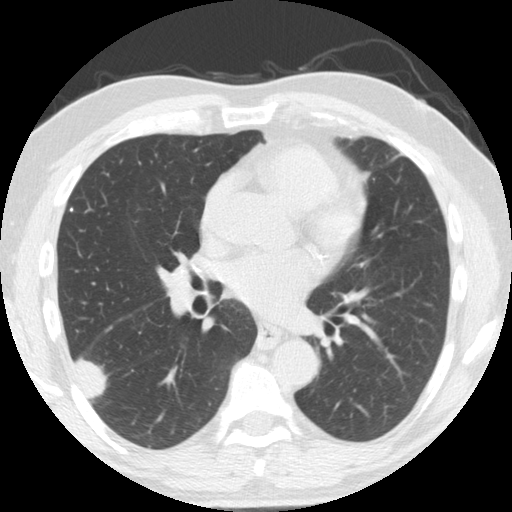
Low-dose screening chest CT, one axial slice. Reconstruction kernel STANDARD. Lung window (W 1500 / L -600 HU). 2.5 mm slice thickness. 512 × 512 image matrix, field of view 341 × 341 mm.
Annotated regions visible in this slice (expert manual segmentation):
- lesion 1 (tumor, lower lobe of right lung): bounding box <75,358,107,399> (left, top, right, bottom; pixels)